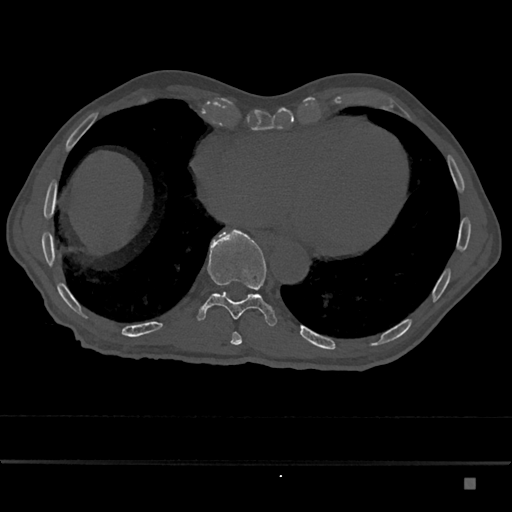
CT including the spine, one axial slice. Slice 742 of 797 in the series (ordered by position). 120 kVp. Bone window (W 1800 / L 400 HU). 512 × 512 image matrix, field of view 390 × 390 mm. Male patient, age 72 years. Case-level facts recorded for this patient, not image findings: primary cancer: prostate.
Structures marked on this image (semi-automatically segmented with operator editing):
- T10 vertebra: bounding box (x1, y1, x2, y2) in pixels: (198, 229, 277, 326)
- T9 vertebra: (231, 332, 242, 345)